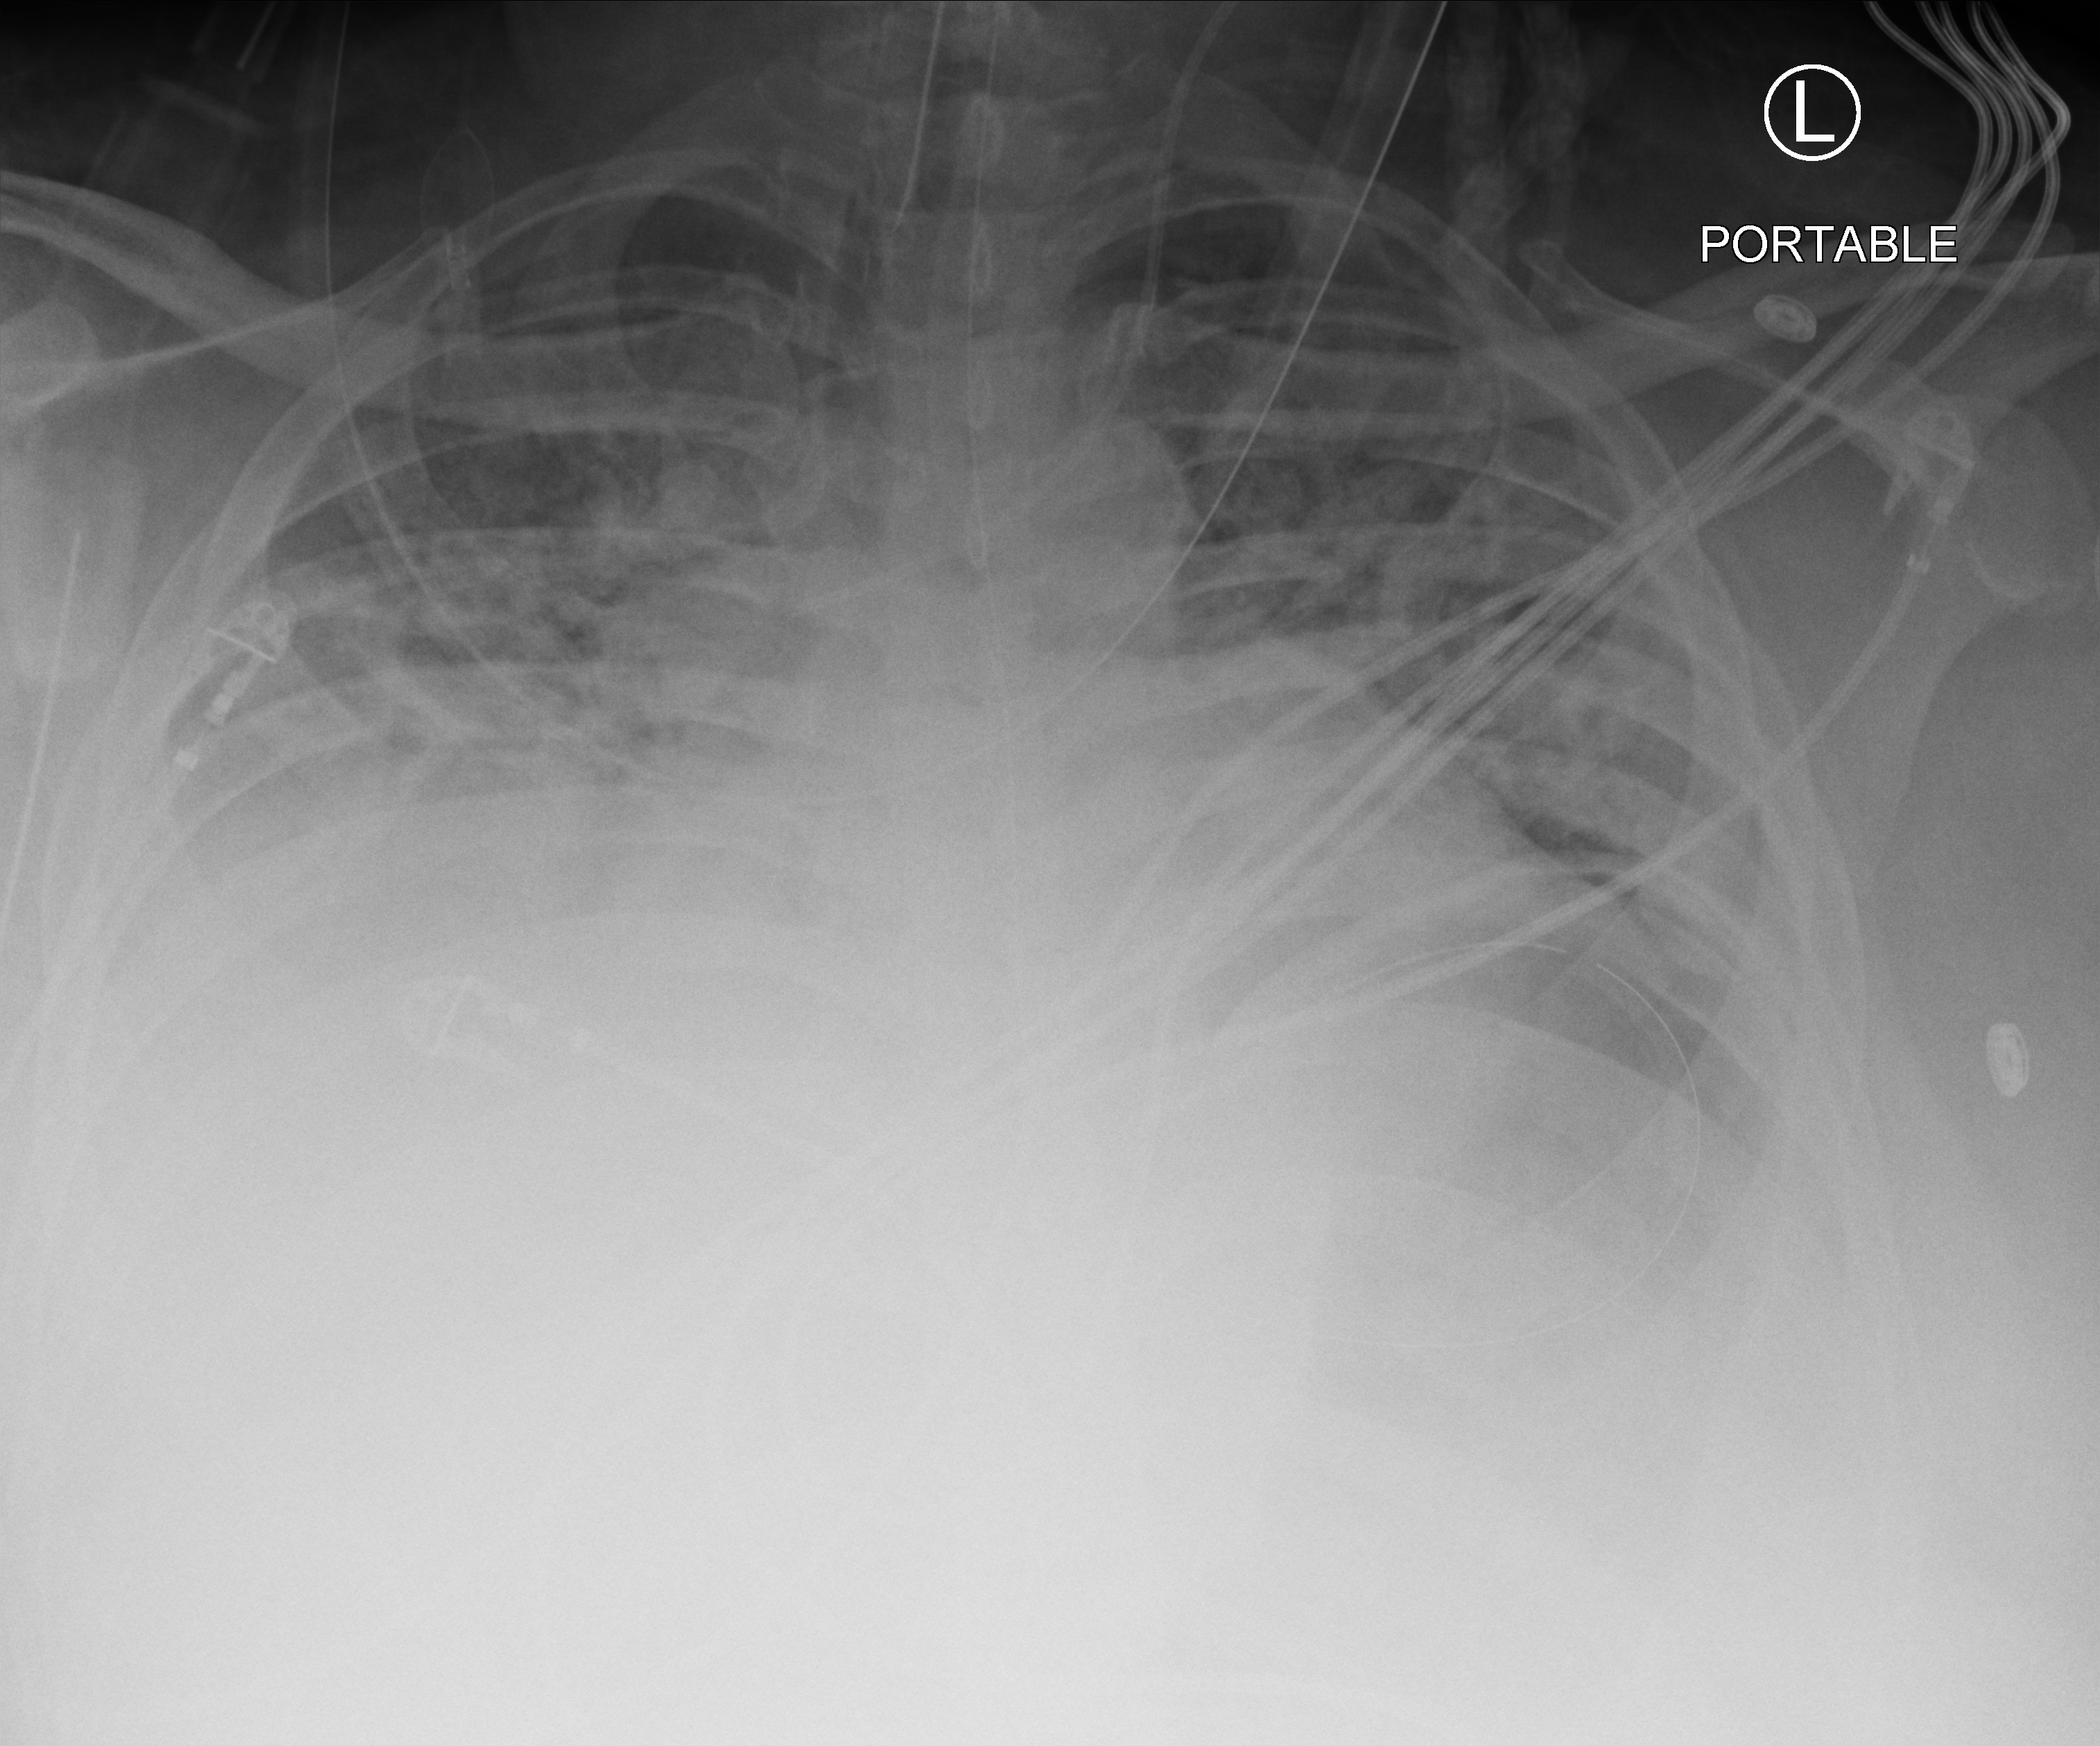
Chest X-ray (portable); anteroposterior (AP) projection. Male patient hospitalised with COVID-19, age 18–59 years.
Hospital-stay facts (about this admission, not read from this image; timing relative to this image not recorded):
- mechanically ventilated during this hospital stay: yes
- other chronic lung disease (admission record): yes
- smoking status (admission record): never